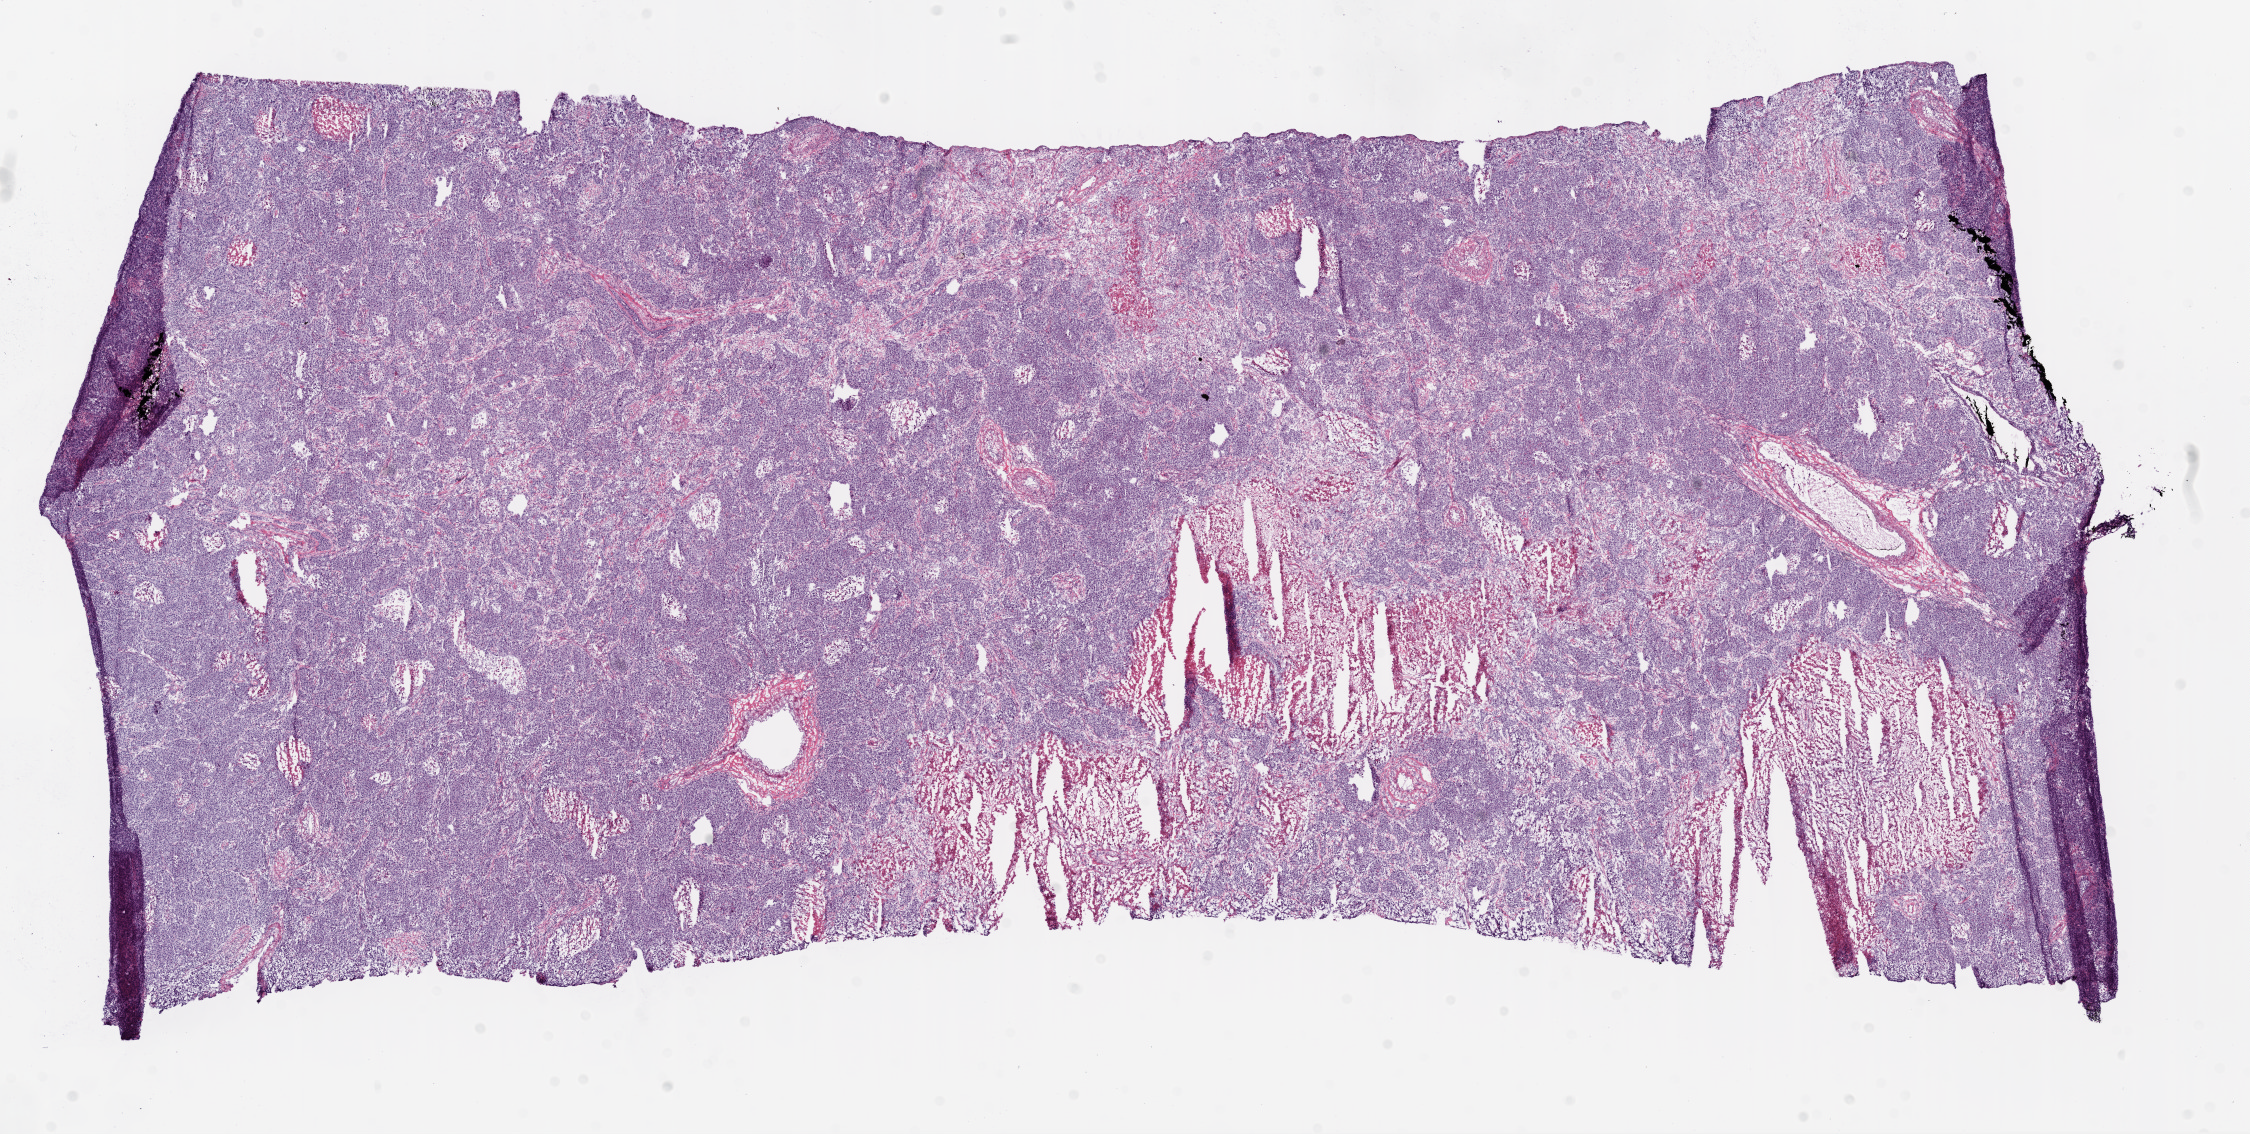
H&E-stained whole-slide image — shown as a low-resolution overview of the whole scanned area (about 18.1 x 9.1 mm); frozen section from the bottom of the tissue portion; primary tumour sample from the lung. Male patient; age at initial diagnosis 68 years. Slide review estimates, as recorded: tumour cells 80%, tumour nuclei 90%, normal cells 5%, stromal cells 5%, necrosis 10%.
* diagnosis: Adenocarcinoma, NOS (lower lobe, lung)
* AJCC pathologic stage: IIIA